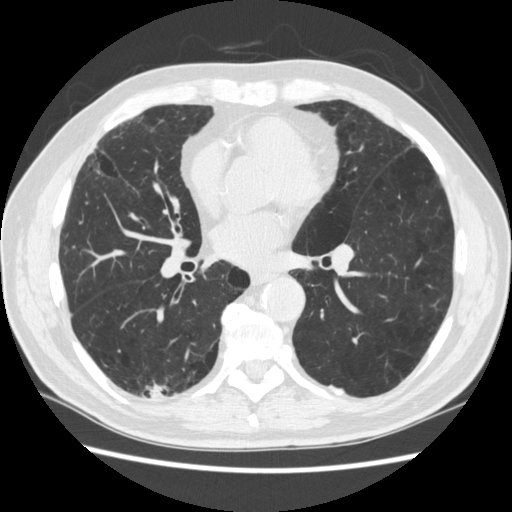
Low-dose screening chest CT, axial slice, third screening round (two years after baseline), lung window (W 1500 / L -600 HU), 1.25 mm slice thickness. Male participant, aged 70 years at enrolment. Former smoker at enrolment.
- Expert reader's lesion annotation, bounding box [x1, y1, x2, y2] px = [120, 361, 186, 422].
- The screening reader recorded 4 non-calcified nodules or masses ≥4 mm on this exam (right lower lobe, right lower lobe, left lower lobe, left lower lobe); which of them this box marks is not recorded.